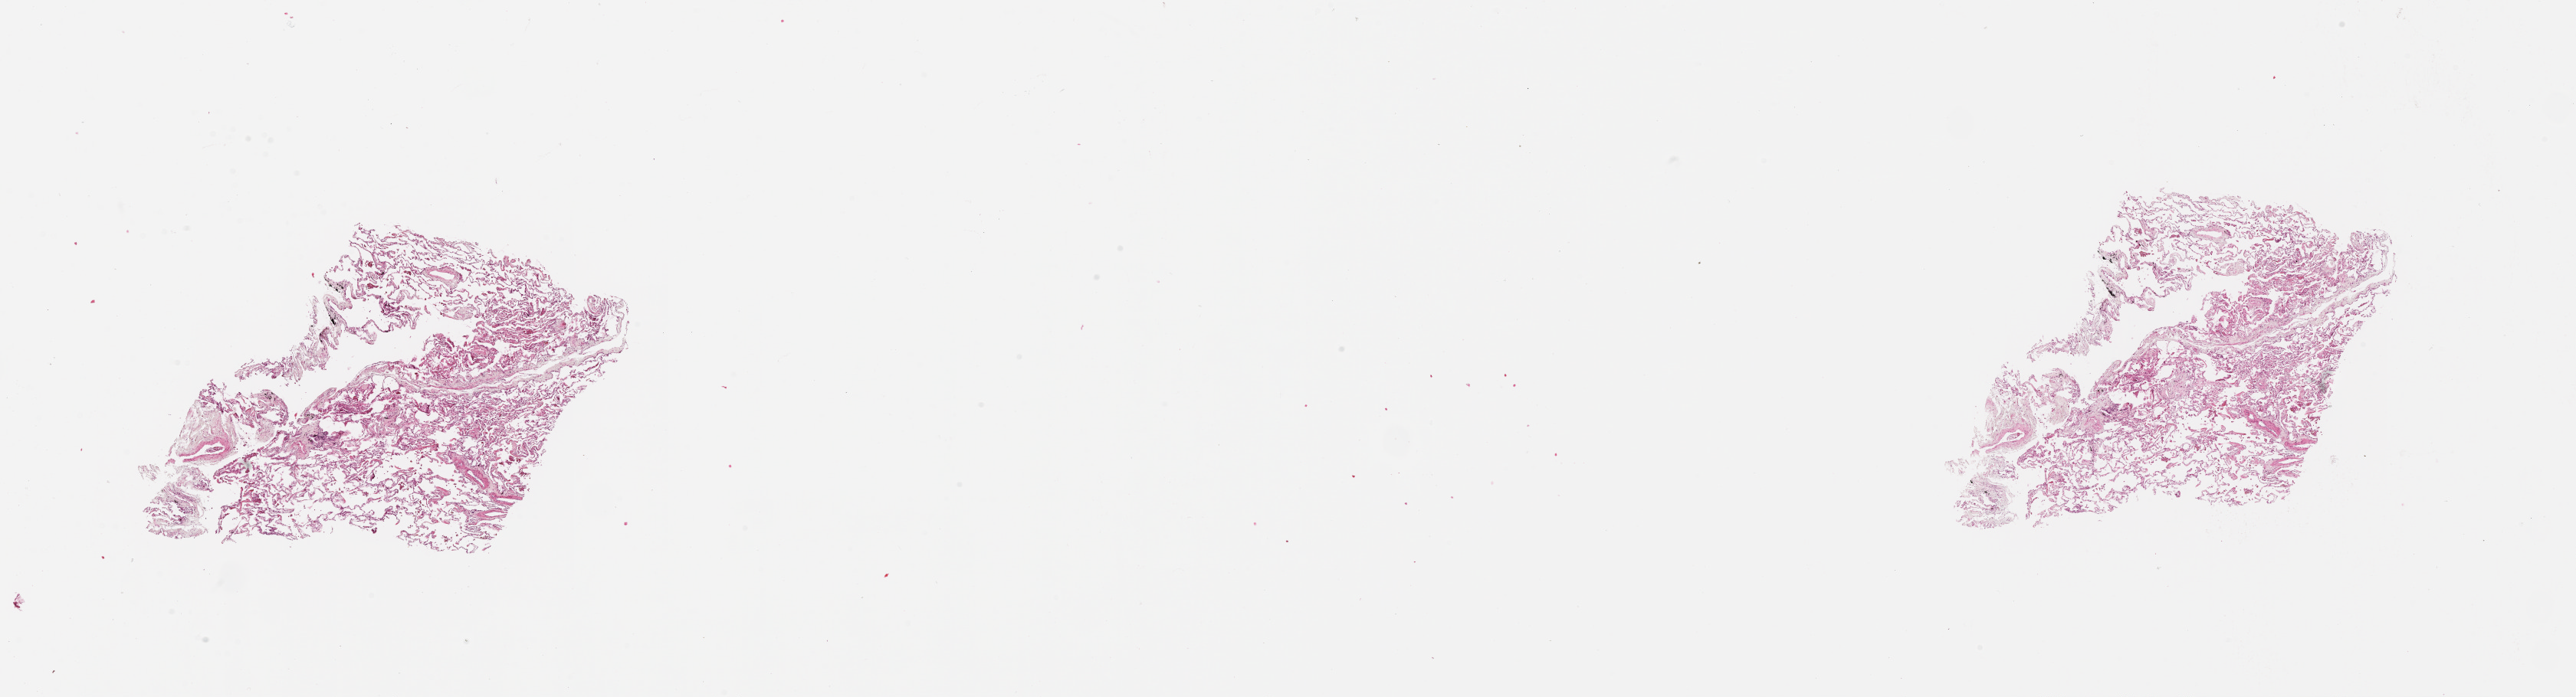
Hematoxylin and eosin (H&E) stained whole-slide image — whole scanned area (about 27.1 x 7.3 mm) shown as a low-resolution overview; lung, normal (non-tumour) tissue. 70-year-old female patient.
* this section: normal (non-tumour) tissue from the same patient
* patient diagnosis (cohort enrolment): squamous cell carcinoma (lung)